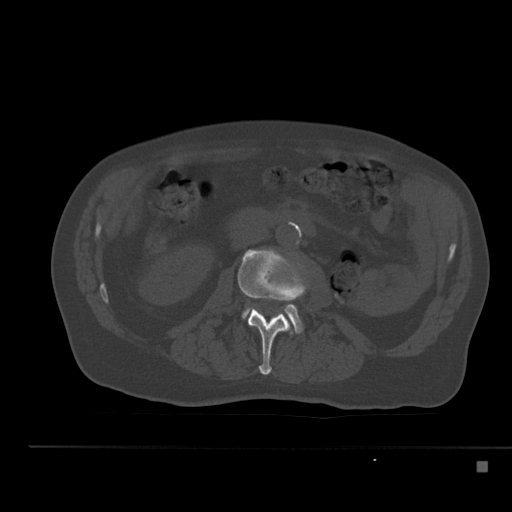
CT including the spine, one axial slice; position 179 of 517 along the scan axis; bone window (W 1800 / L 400 HU); 512 × 512 image matrix, field of view 408 × 408 mm. Patient: male, 70 years. Case-level facts recorded for this patient, not image findings: primary cancer: renal; vertebrae with lytic lesions (as recorded): T4, T6, T10, T12, L3, L4, L5.
Outlined on this slice (semi-automatically segmented with operator editing):
- L2 vertebra: box from (x=238, y=249) to (x=308, y=375) px
- L3 vertebra: (x=242, y=304)–(x=302, y=333)